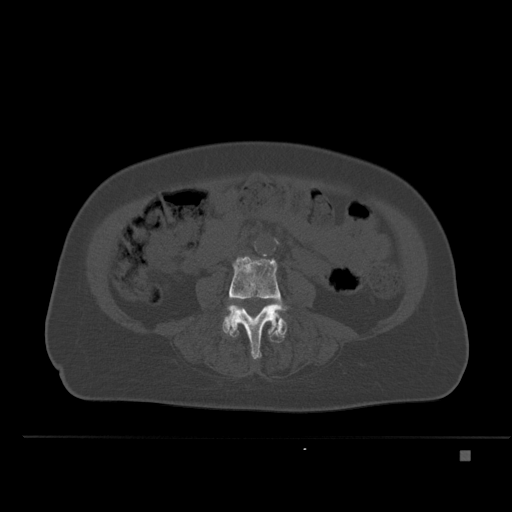
CT including the spine, one axial slice; slice 177 of 477 in the series (ordered by position); bone window (W 1800 / L 400 HU); 1.5 mm slice thickness; 512 × 512 image matrix, field of view 422 × 422 mm. Patient: female, 74 years. From the clinical record (not read from this slice): primary cancer: colon.
Outlined on this slice (semi-automatic segmentation, software-assisted and operator-edited):
- L4 vertebra: bounding box [x1, y1, x2, y2] px = [226, 256, 290, 359]
- L5 vertebra: [222, 311, 287, 343]